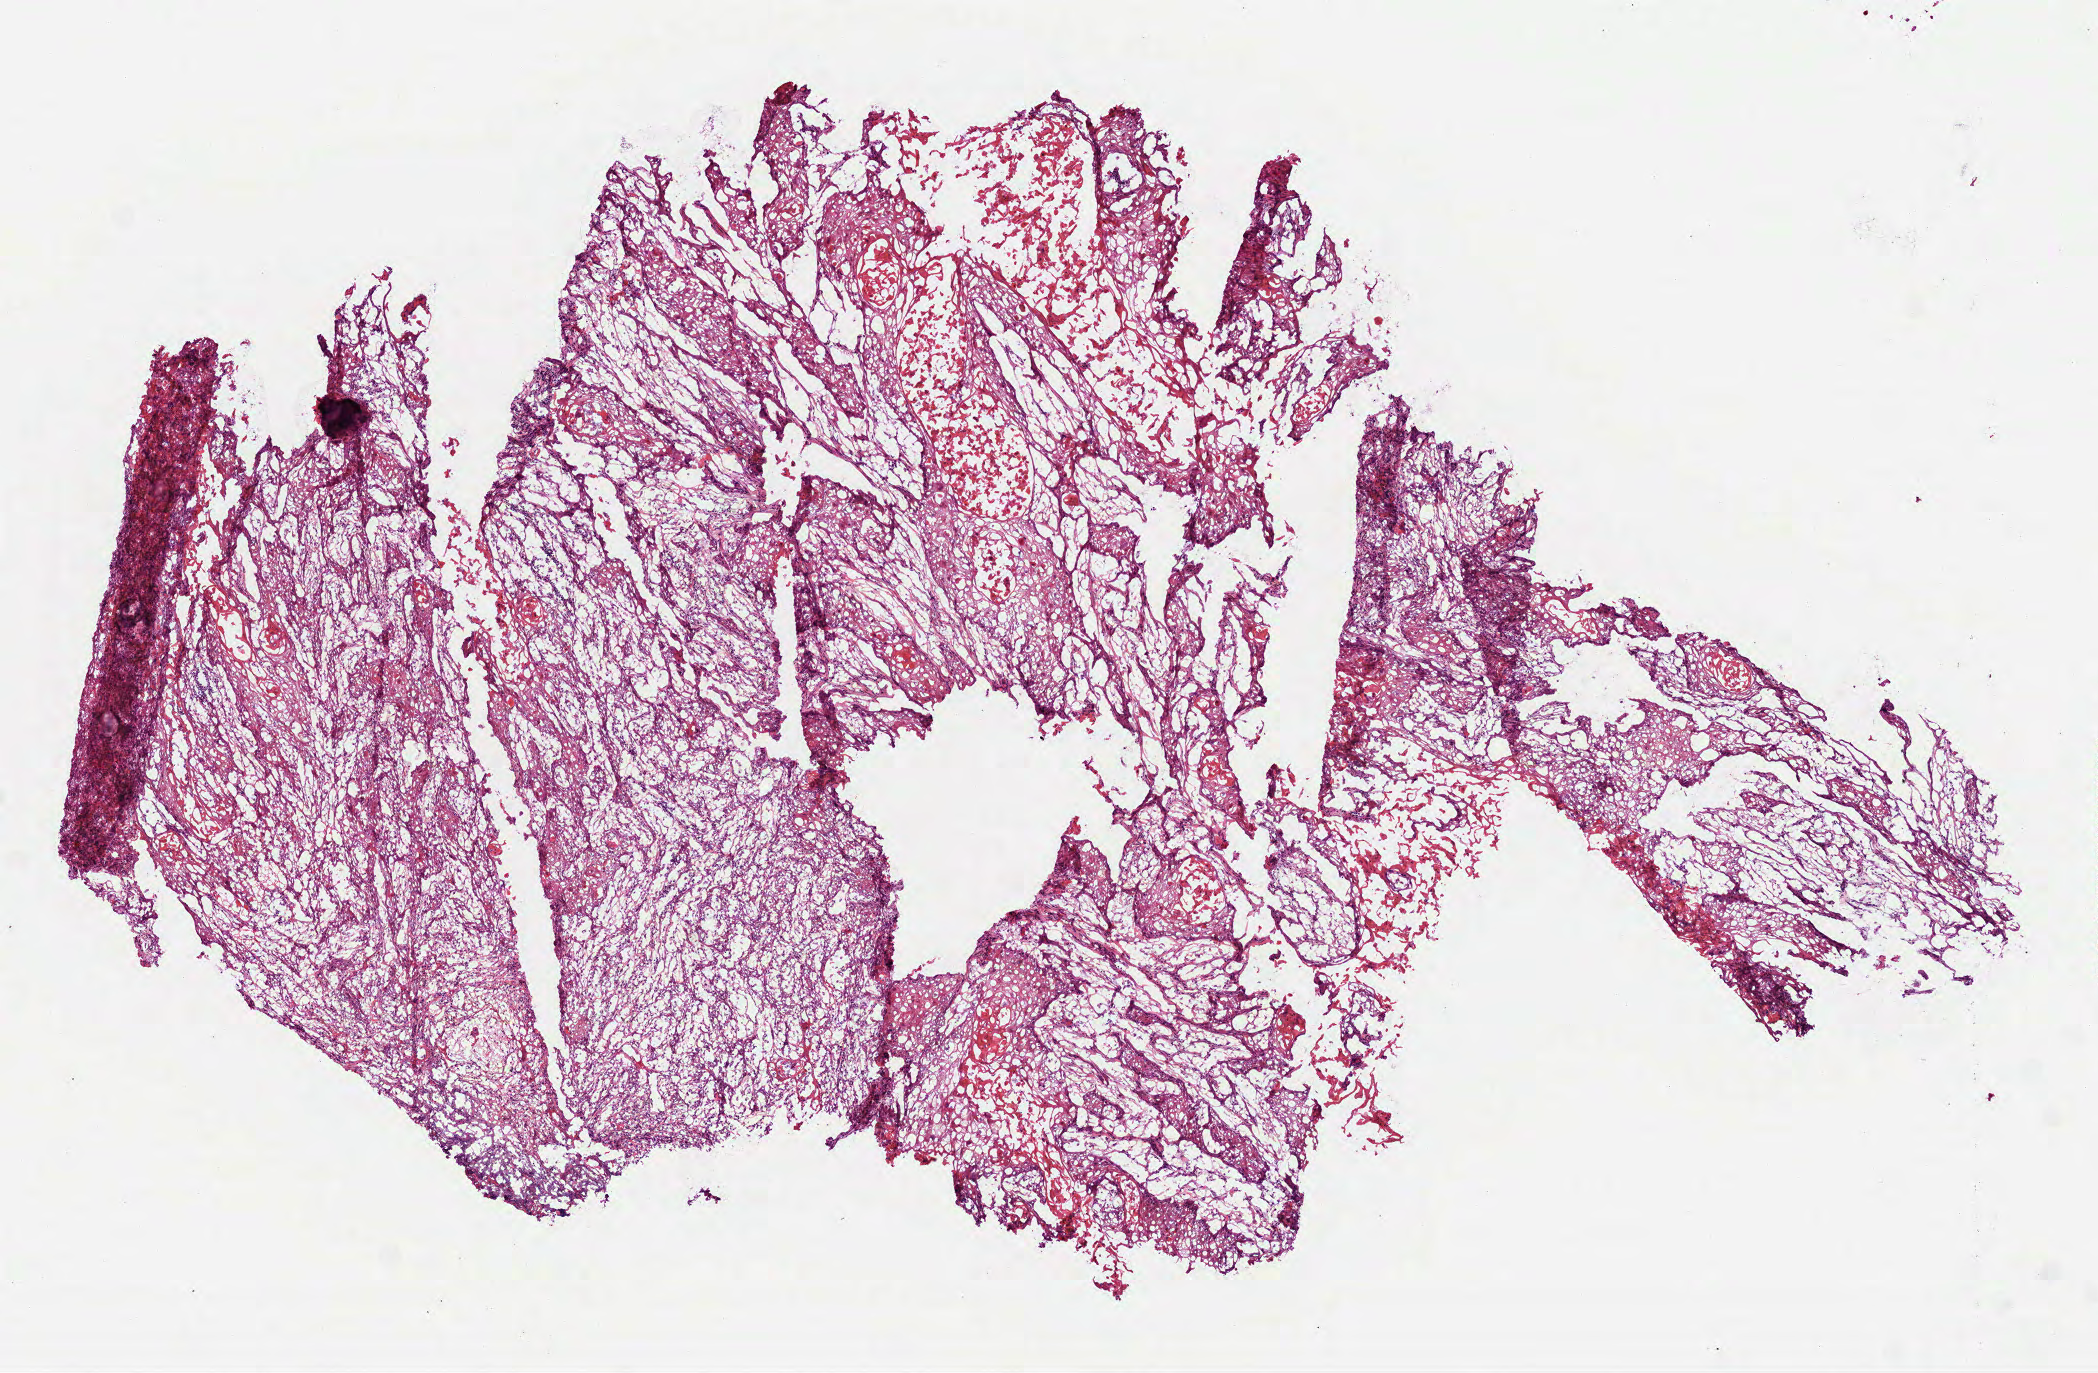
Whole-slide histology image, H&E — low-resolution overview of the scanned area, about 8.5 x 5.5 mm; frozen section from the top of the tissue portion; sample: primary tumour, head and neck. Female, age 62 years at initial diagnosis. Histologic grade: G2 (moderately differentiated). Pathologist review of this section (percent, as recorded): tumour cells 75%, tumour nuclei 75%, normal cells 0%, stromal cells 25%, necrosis 0%.
• AJCC pathologic stage: IVA (7th edition)
• histologic diagnosis: Squamous cell carcinoma, NOS (overlapping lesion of lip, oral cavity and pharynx)
• TNM: T4a N0